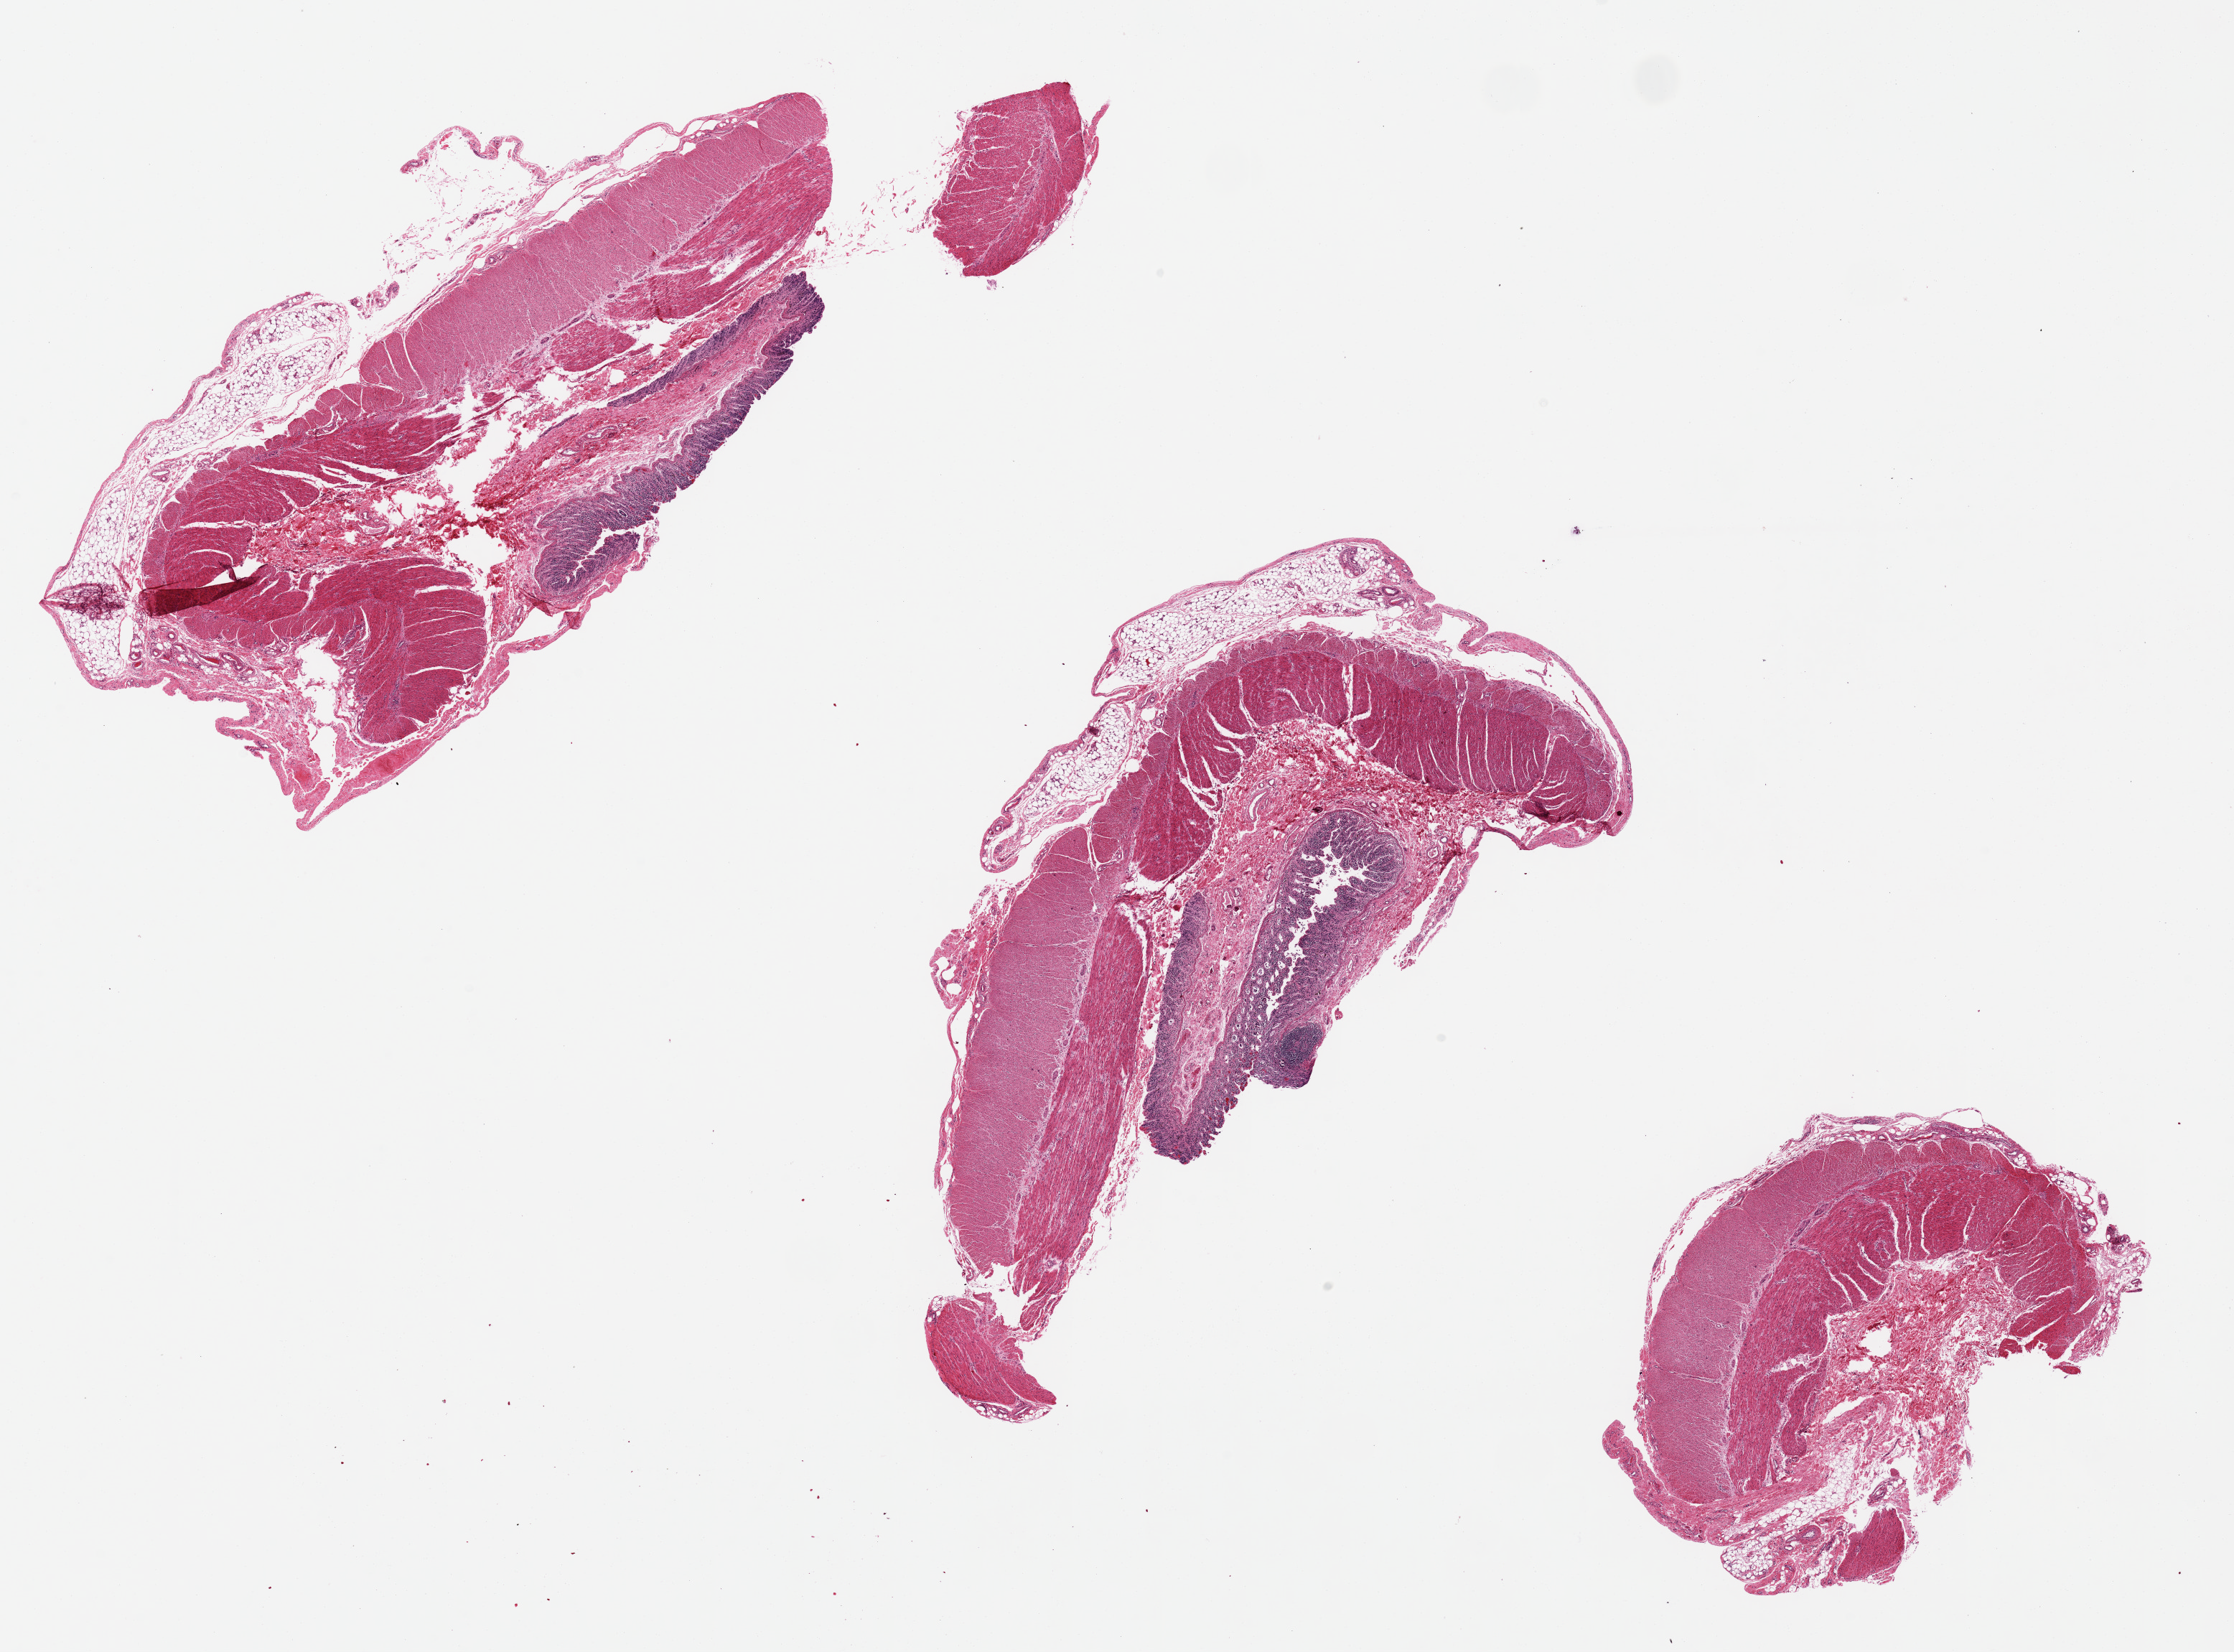
H&E whole-slide image — a low-resolution overview of the entire scanned area, about 24.6 x 18.2 mm (from a 20x scan); PAXgene-fixed paraffin-embedded (PFPE) section; sampled site (target tissue): stomach; tissue donor sample.
Reviewer comment on this tissue sample: Epithelium totally gone from mucosa; only lamina propria elements remain.